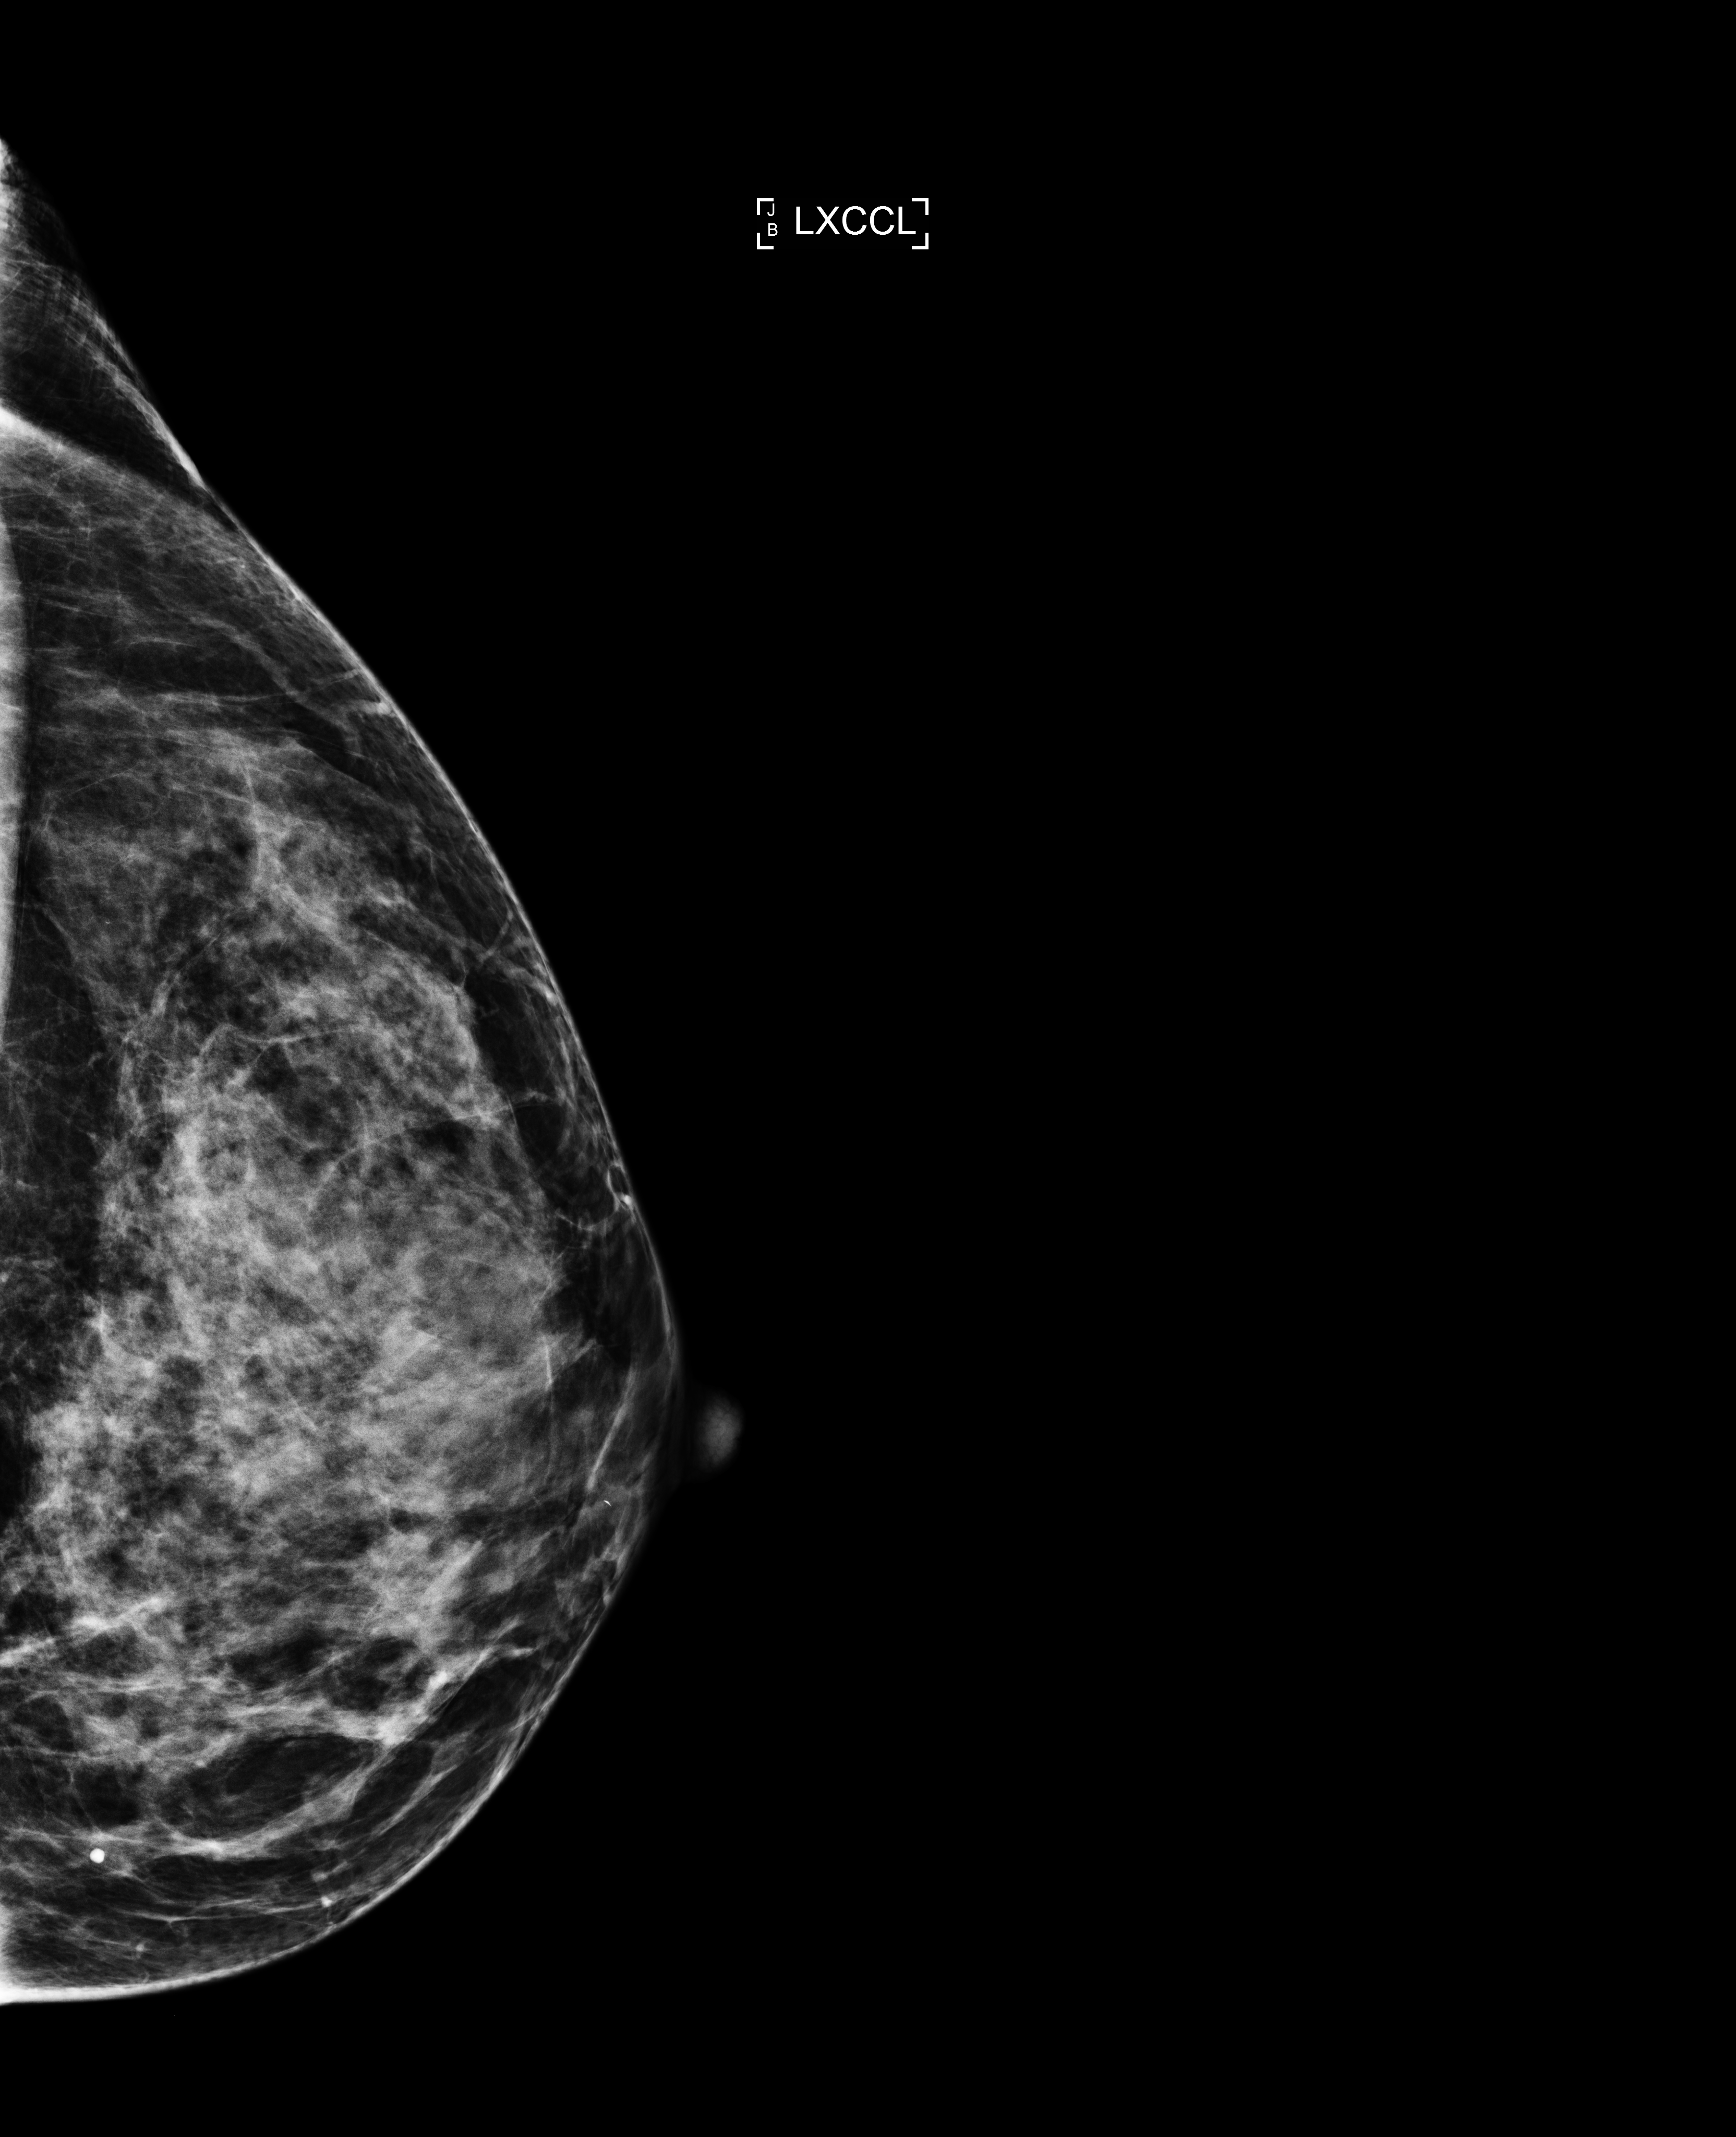
Annual screening mammography examination; compressed breast thickness 67 mm. Patient aged 42 years (female).
Image type: full-field digital mammogram. Breast: left. Projection: exaggerated CC view (lateral).